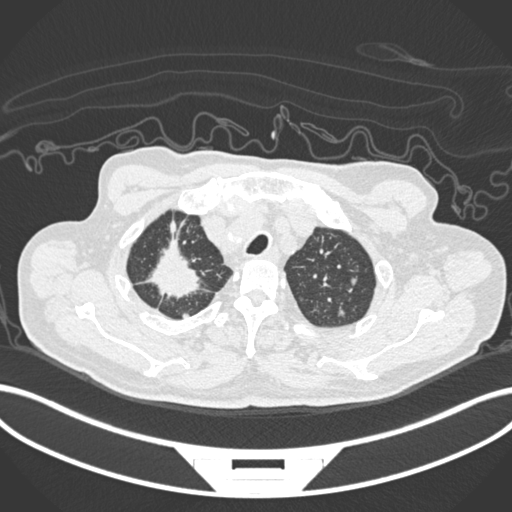
Chest CT, one axial slice. Slice 189 of 207 in the series (ordered by position). Reconstruction kernel B30f. 120 kVp. Lung window (W 1500 / L -600 HU). 1 mm slice thickness. 512 × 512 image matrix, field of view 400 × 400 mm. Male patient, age 69 years. Case-level facts recorded for this patient, not image findings: clinical TNM (as recorded): T1c N1 M1.
Outlined on this slice (bounding box drawn by a radiologist):
- lung tumour (recorded histology: adenocarcinoma): bounding box (x1, y1, x2, y2) in pixels: (143, 241, 208, 299)